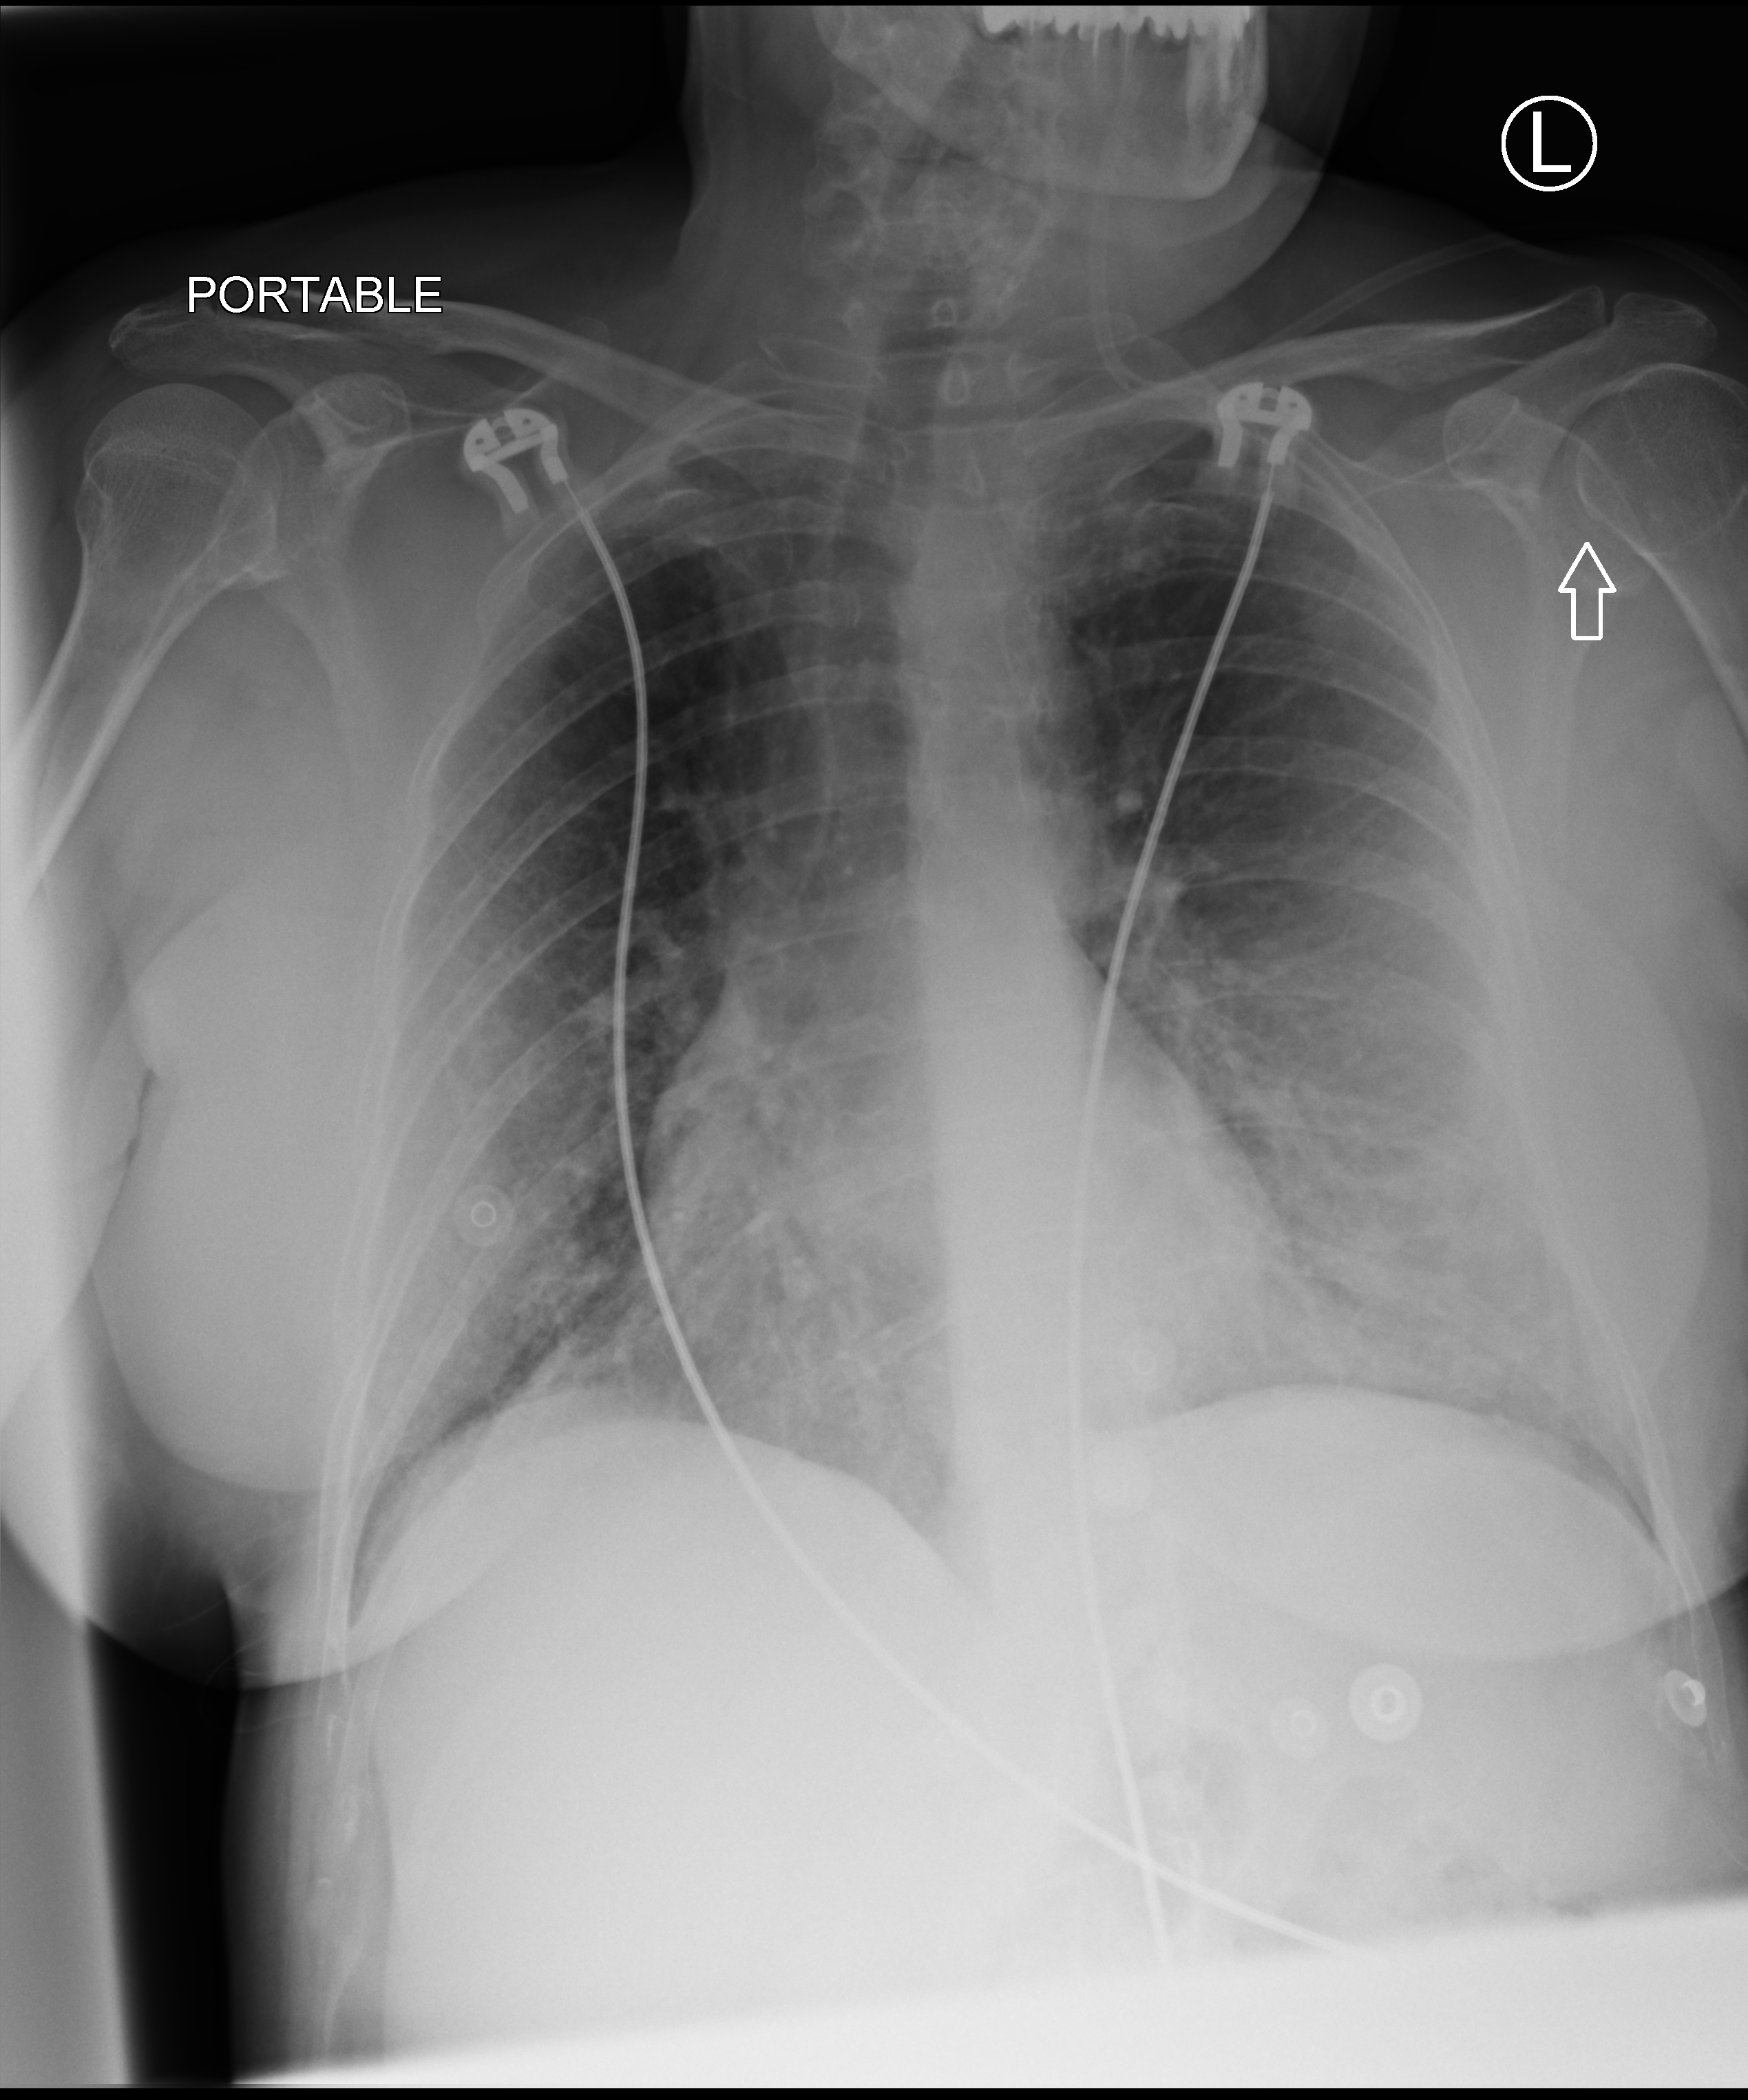
Bedside chest radiograph (computed radiography), anteroposterior (AP) projection. Patient hospitalised with COVID-19; female, aged 60–74 years.
Hospital-stay facts (about this admission, not read from this image; timing relative to this image not recorded): mechanically ventilated during this hospital stay: no; admitted to intensive care during this hospital stay: no.